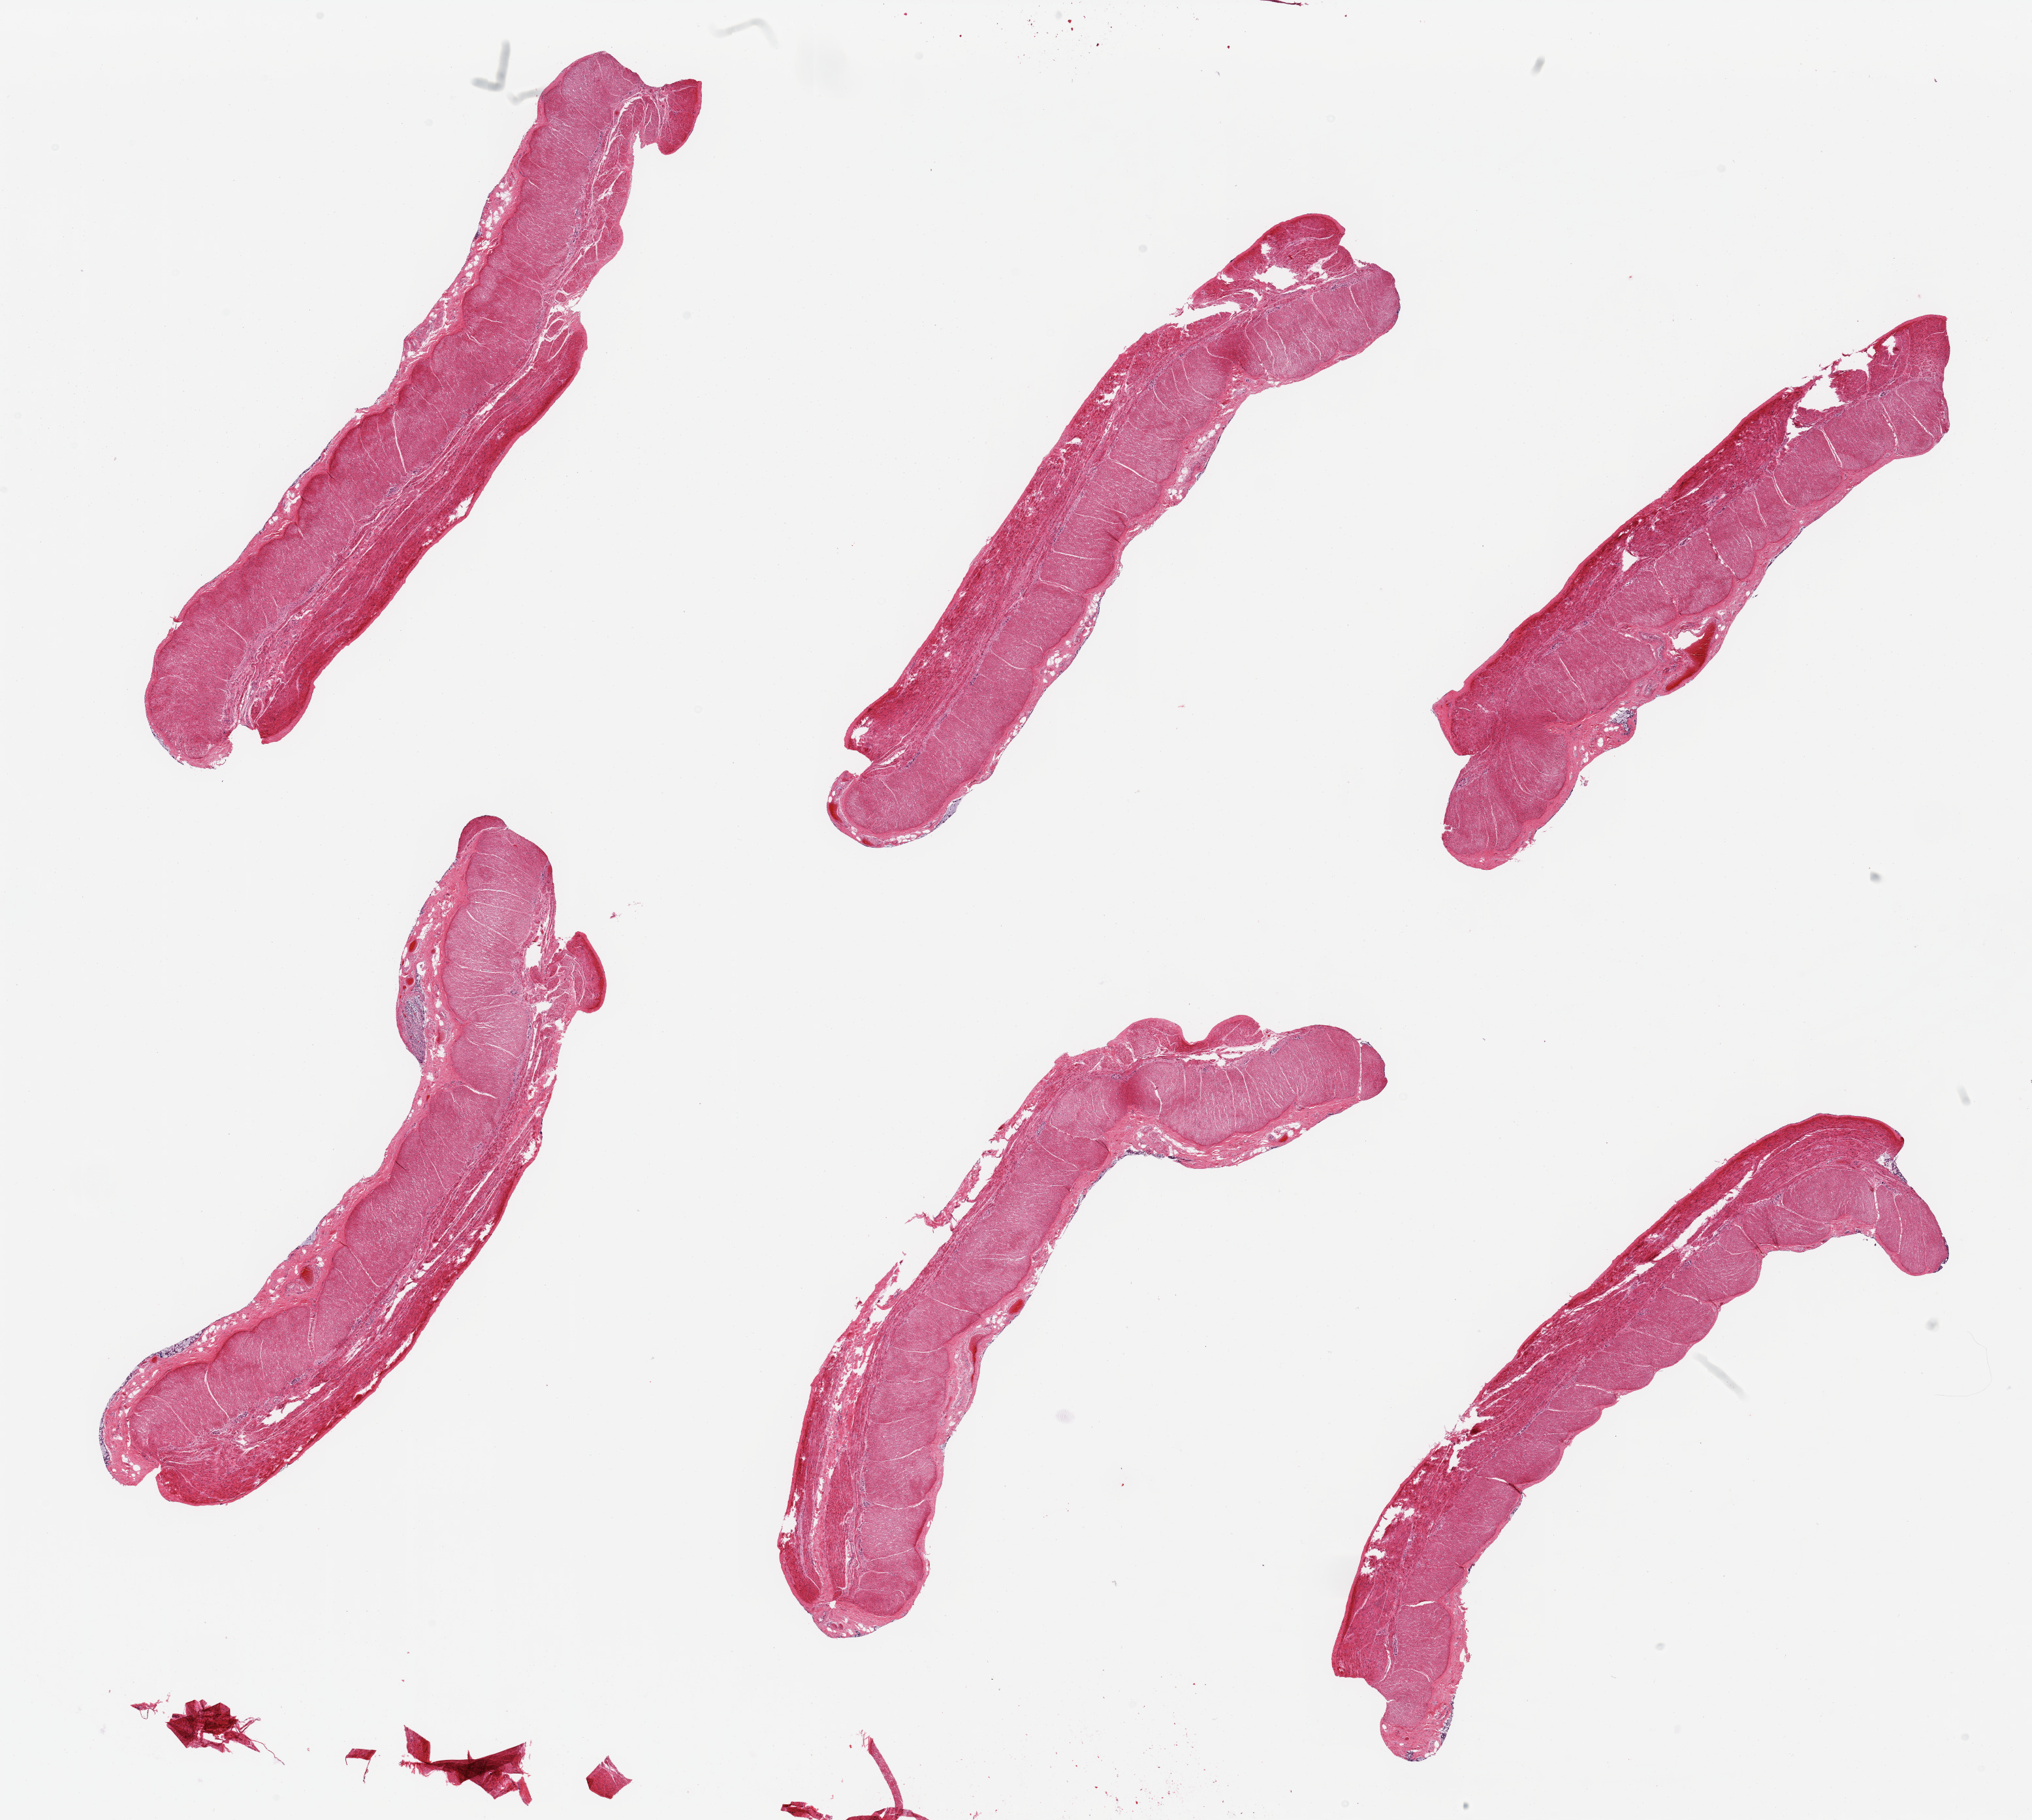
Whole-slide image, haematoxylin and eosin stain, a low-resolution overview of the entire scanned area, about 24.6 x 22.0 mm (acquisition: 20x scan). PAXgene-fixed, paraffin-embedded tissue. Target tissue: sigmoid colon. Donor tissue sample. Donor sex: male.
Reviewer comment on this tissue sample: 6 pieces; well dissected muscularis.